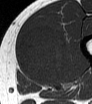
MRI of an extremity soft-tissue mass, one axial slice. Position 25 of 62 along the scan axis. MR volume resampled by the dataset authors to the PET/CT grid (not the native acquisition matrix). 3.27 mm slice thickness. 92 × 104 image matrix, field of view 90 × 102 mm. Male patient. Case-level facts recorded for this patient, not image findings: histological type: mixoid liposarcoma; grade: low; site of the primary tumour: left thigh.
Structures marked on this image (expert contour drawn on MRI and transferred to this co-registered scan by the dataset authors):
- gross tumour volume (mass): bounding box (x1, y1, x2, y2) in pixels: (19, 24, 67, 84)